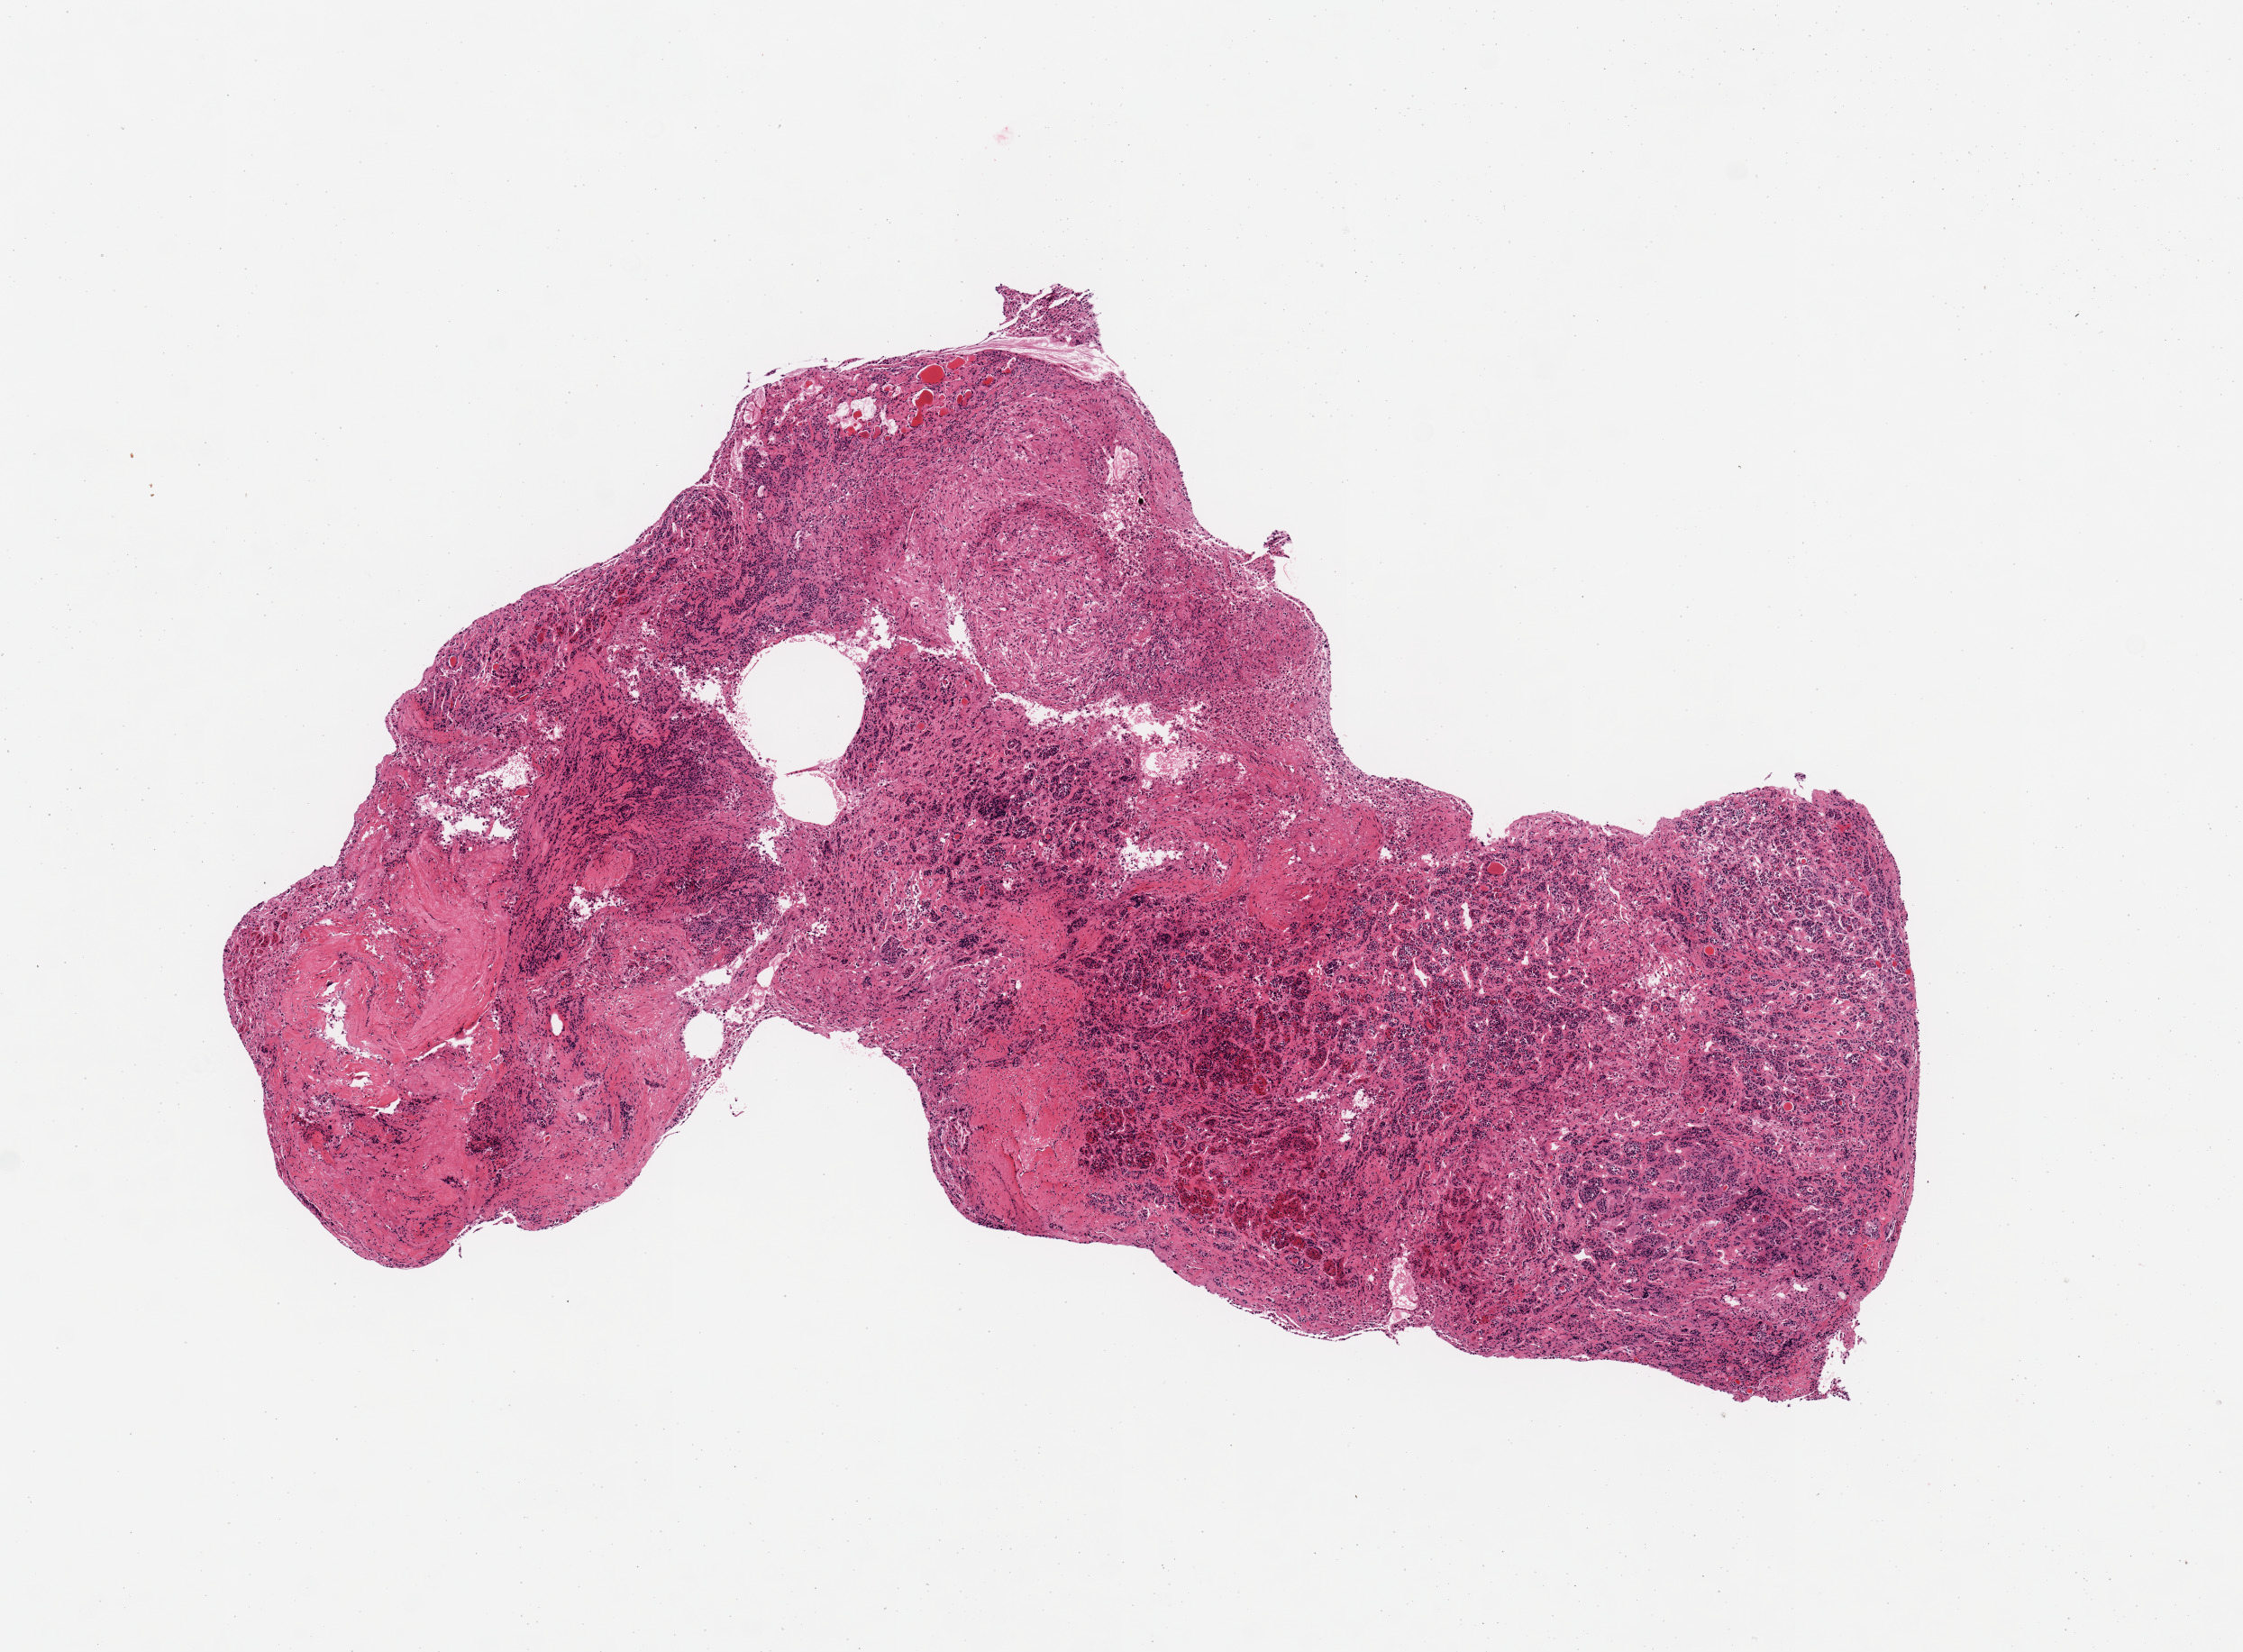
Haematoxylin and eosin whole-slide image — a low-resolution overview of the entire scanned area, about 9.8 x 7.2 mm, PAXgene-fixed, paraffin-embedded tissue, section of pituitary (target tissue), donor tissue sample. Male donor.
Reviewer comment on this tissue sample: 1 piece, ~ 10-15% neurohypophysis, rest adenohypophysis.